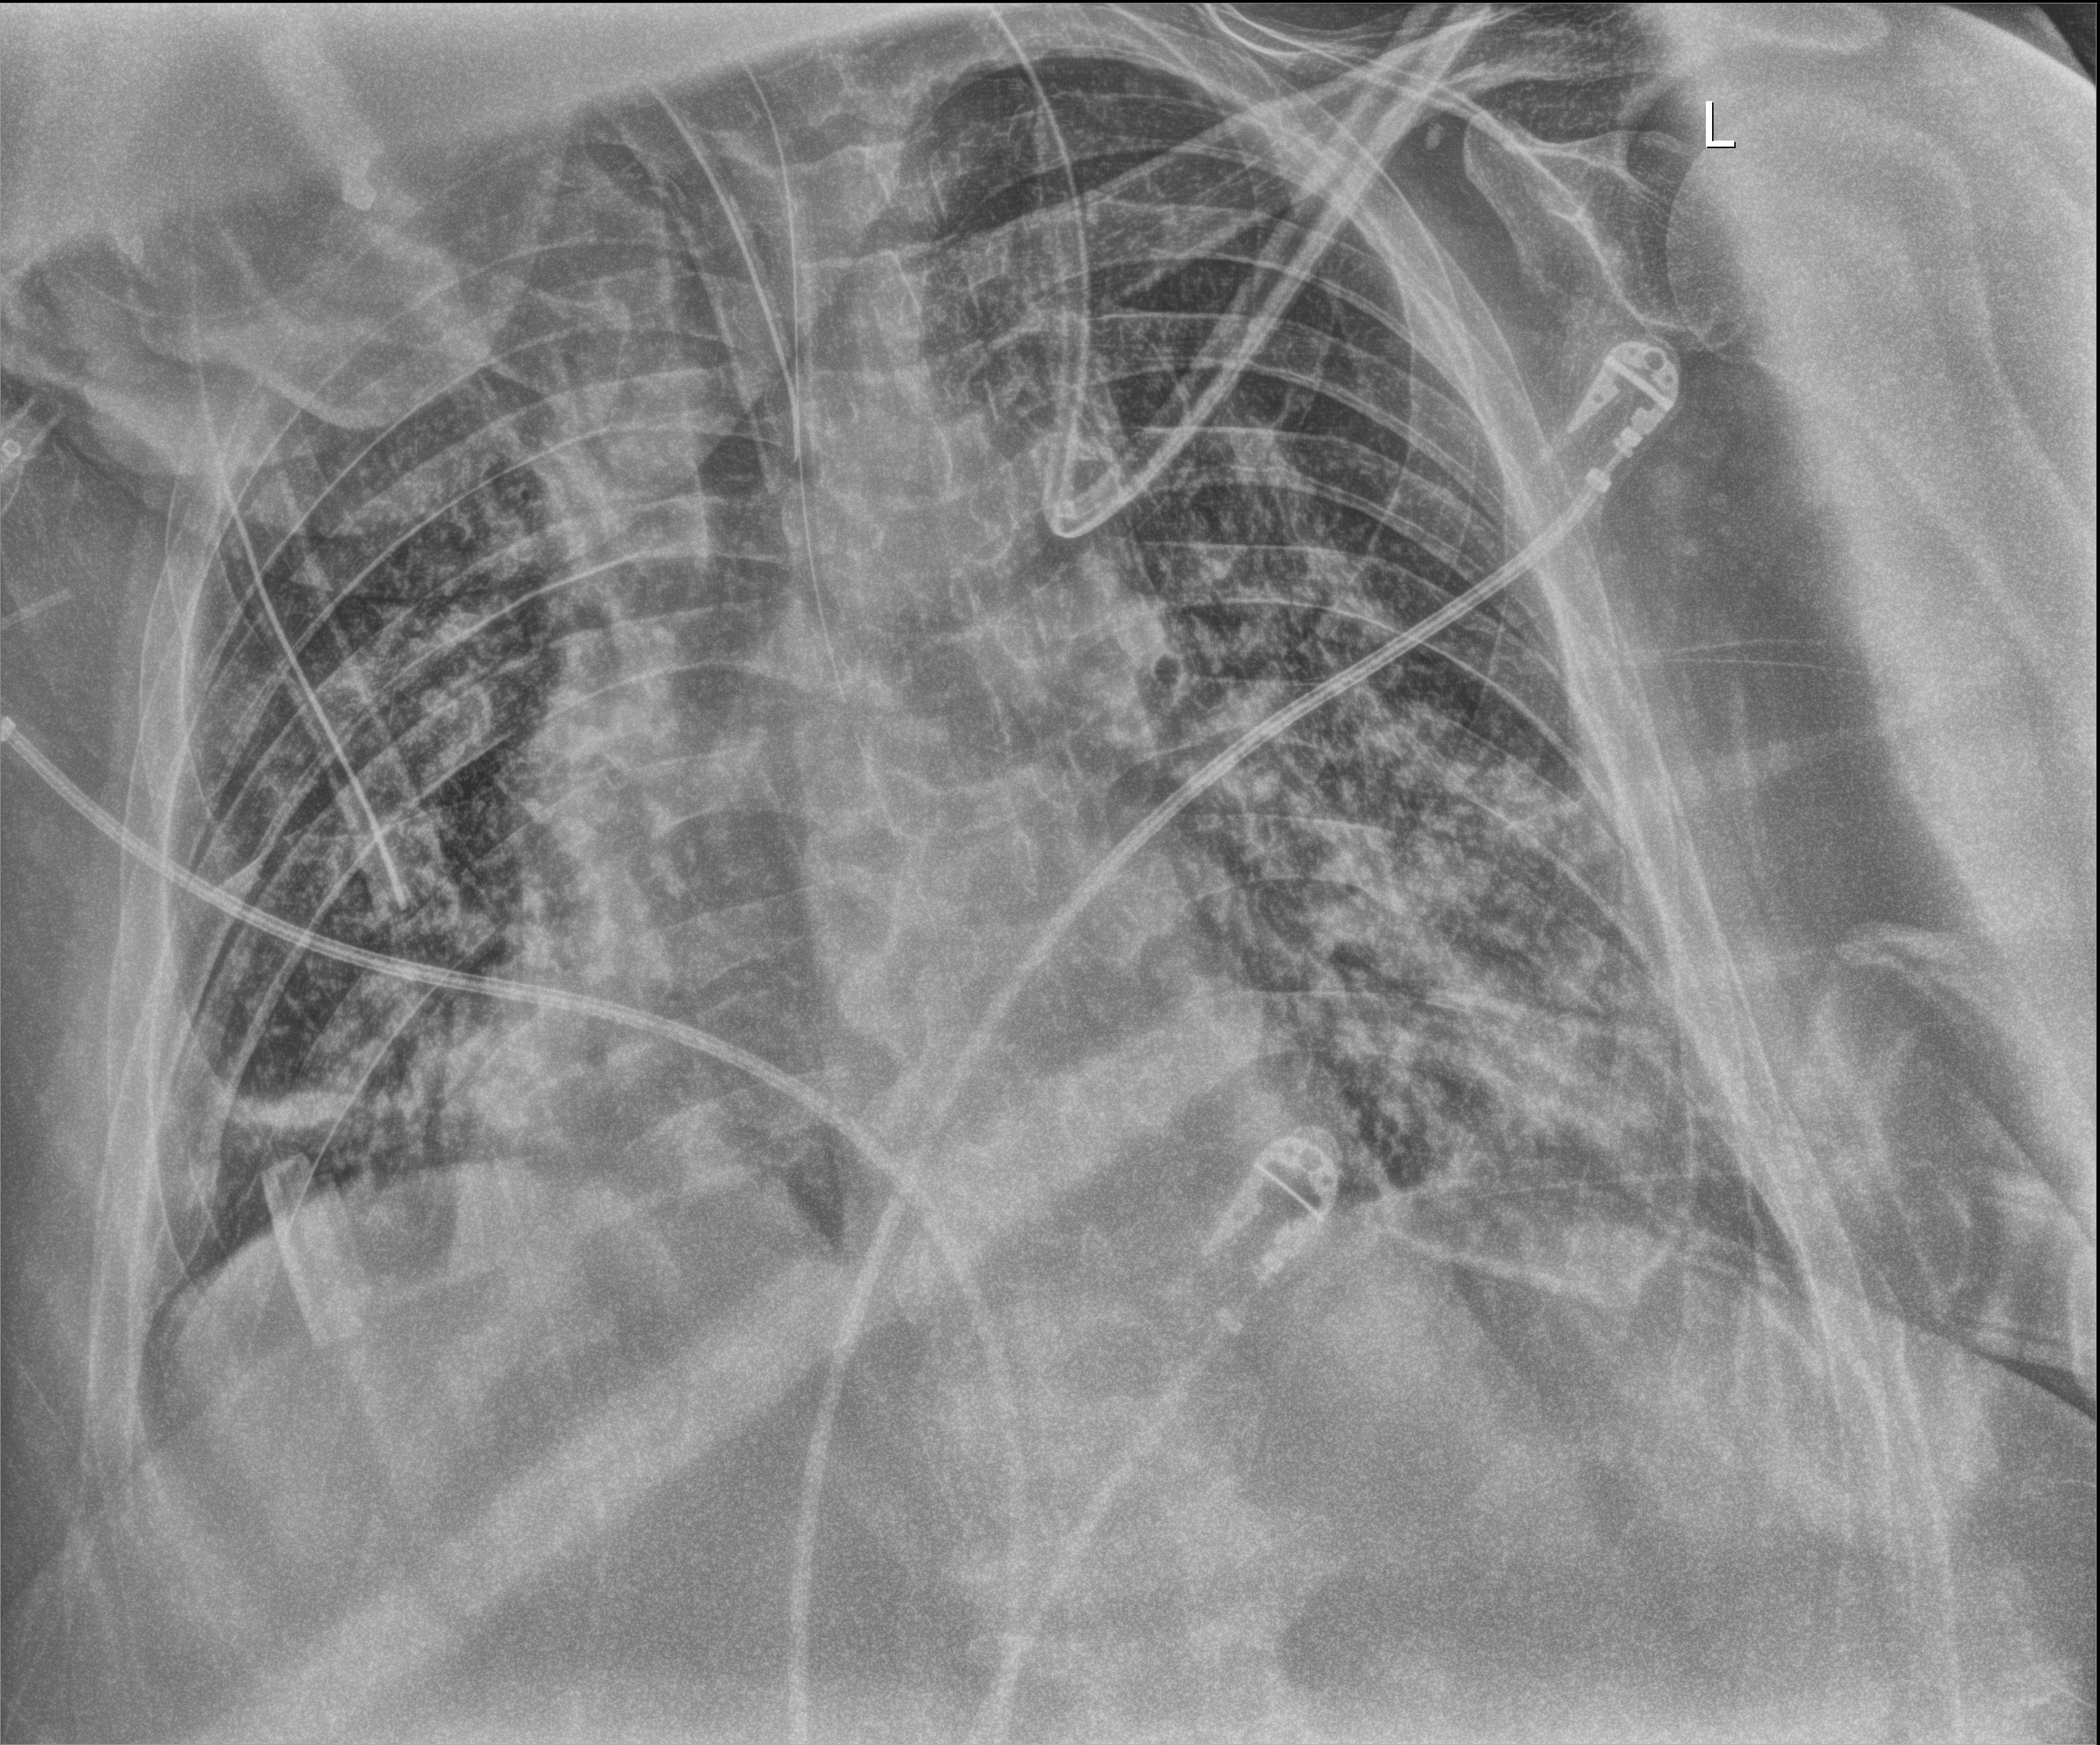
Chest radiograph (digital radiography), anteroposterior (AP) projection. Male patient hospitalised with COVID-19, age 60–74 years.
Admission-level facts for this patient (not findings on this image; timing relative to this image not recorded):
- diabetes (admission record): no